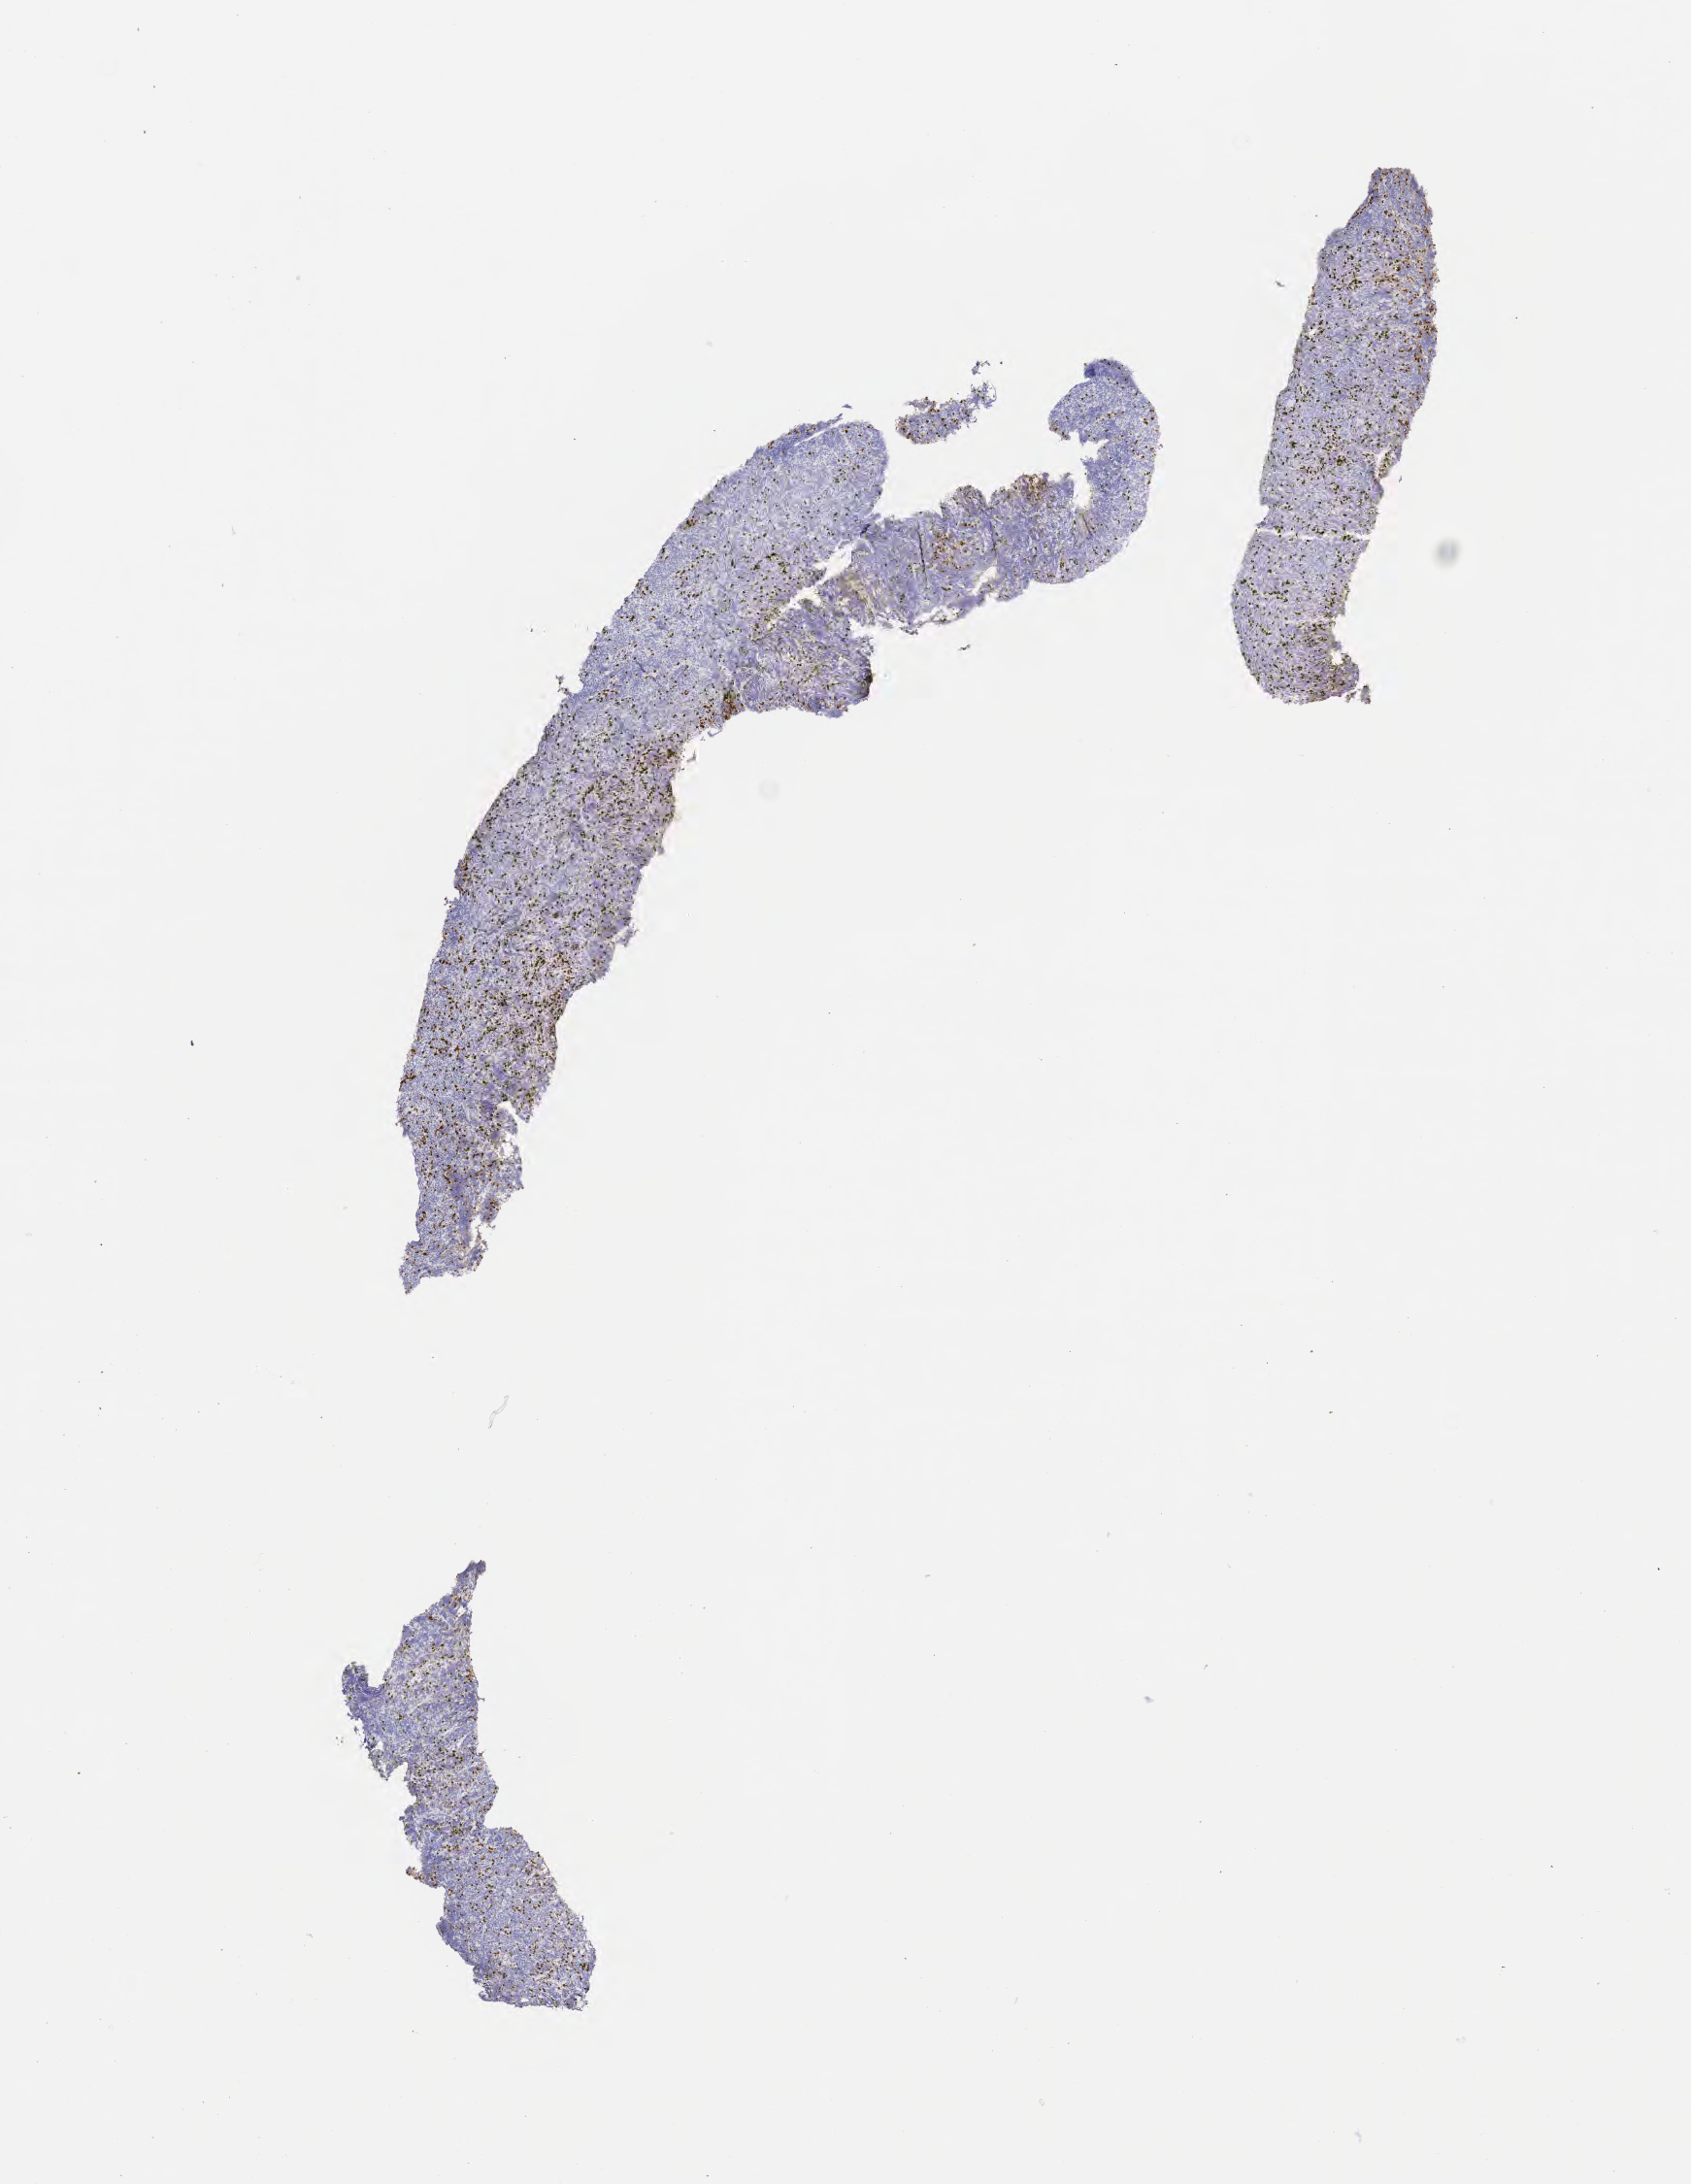
Whole-slide image, immunohistochemical stain for CD3, low-resolution overview of the scanned area, about 7.0 x 9.1 mm. Tumor tissue. Patient: male, aged 10.
Histologic diagnosis: Diffuse large B-cell lymphoma, NOS.